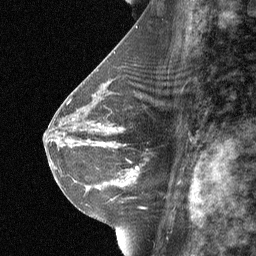
Breast MRI (dynamic contrast-enhanced), one sagittal slice; slice 36 of 64 in the series (ordered by position); dynamic contrast-enhanced study with each time point stored as its own series, time point 2 of 3 at this slice position (early post-contrast, ordered by acquisition time); 1.5 T; TE 4.8 ms, TR 27 ms; 256 × 256 image matrix, field of view 180 × 180 mm. Female patient, age 42 years. From the clinical record (not read from this slice): setting: breast cancer imaged before/during neoadjuvant chemotherapy; receptor status: triple-negative.
Outlined on this slice (semi-automatic segmentation, software-assisted and operator-edited):
- analysis volume of interest (the breast-tissue region the enhancement analysis was run in; not a lesion): bounding box [x1, y1, x2, y2] px = [99, 117, 174, 187]
- tumour enhancement mask (voxels above the 90 % enhancement threshold inside the analysis volume of interest): [119, 127, 138, 186]